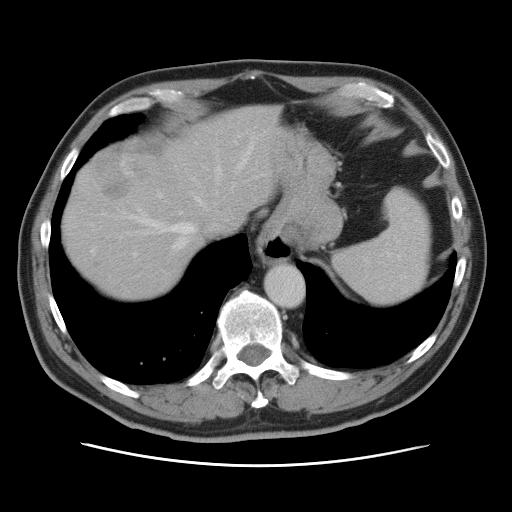
Contrast-enhanced abdominal CT, one axial slice. Slice 65 of 80 in the series (ordered by position). 120 kVp. Soft-tissue window (W 400 / L 40 HU). 5 mm slice thickness. 512 × 512 image matrix. Male patient, age 69 years. Case-level facts recorded for this patient, not image findings: diagnosis: colorectal cancer liver metastases, imaged before liver resection; multiple liver metastases: no; largest metastasis: 5 cm; disease in both lobes: yes.
Structures marked on this image (manually delineated by an expert):
- hepatic veins: box from (x=91, y=135) to (x=256, y=253) px
- liver: (x=63, y=106)–(x=278, y=298)
- planned liver remnant (the part of the liver to remain after resection): (x=63, y=106)–(x=277, y=298)
- portal vein (with intrahepatic branches): (x=133, y=141)–(x=233, y=257)
- liver metastasis: (x=93, y=153)–(x=144, y=201)